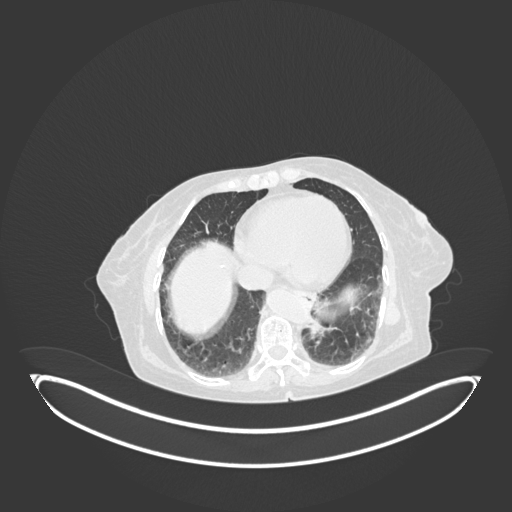
Chest CT, one axial slice; slice 18 of 189 in the series (ordered by position); 120 kVp; lung window (W 1500 / L -600 HU); 1 mm slice thickness; 512 × 512 image matrix, field of view 500 × 500 mm. Female patient, age 82 years. Case-level facts recorded for this patient, not image findings: clinical TNM (as recorded): T1b N0 M1.
Outlined on this slice (bounding box drawn by a radiologist):
- lung tumour (recorded histology: adenocarcinoma): box from (x=307, y=311) to (x=336, y=341) px